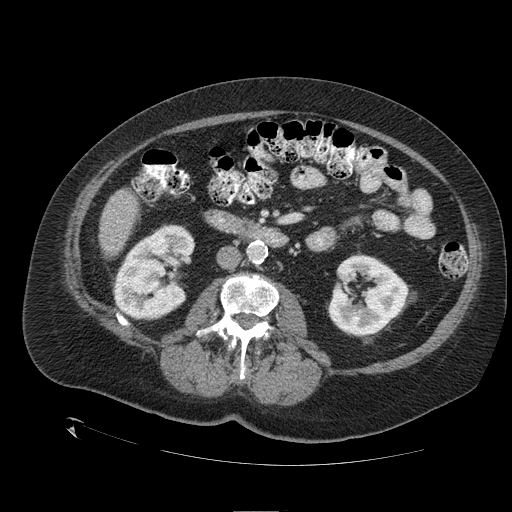
Contrast-enhanced abdominal CT (liver protocol), one axial slice; position 36 of 109 along the scan axis; reconstruction kernel STANDARD; 120 kVp; one of 2 acquisitions stored at this slice position; soft-tissue window (W 400 / L 40 HU); 512 × 512 image matrix. From the clinical record (not read from this slice): diagnosis: hepatocellular carcinoma (patient treated with transarterial chemoembolisation; whether this scan precedes or follows treatment is not stated here); TNM stage (as recorded): Stage-I; Child-Pugh class: A; tumour nodularity: uninodular; tumour size: 4.6 cm.
Annotated regions visible in this slice (semi-automatically segmented with operator editing):
- liver parenchyma outside the tumour (the mass and vessels are separate outlines, so this box may not span the whole liver): bounding box <98,190,138,256> (left, top, right, bottom; pixels)